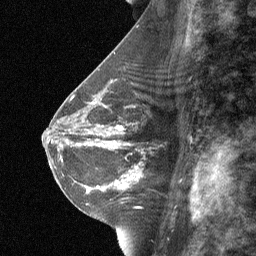
Breast MRI (dynamic contrast-enhanced), one sagittal slice. Position 35 of 64 along the scan axis. Dynamic contrast-enhanced study with each time point stored as its own series, time point 2 of 3 at this slice position (early post-contrast, ordered by acquisition time). 1.5 T. TE 4.8 ms, TR 27 ms. 2 mm slice thickness. 256 × 256 image matrix. Female patient, age 42 years. Case-level facts recorded for this patient, not image findings: setting: breast cancer imaged before/during neoadjuvant chemotherapy; receptor status: triple-negative.
Structures marked on this image (semi-automatically segmented with operator editing):
- analysis volume of interest (the breast-tissue region the enhancement analysis was run in; not a lesion): box from (x=99, y=117) to (x=174, y=187) px
- tumour enhancement mask (voxels above the 90 % enhancement threshold inside the analysis volume of interest): (x=115, y=126)–(x=142, y=187)